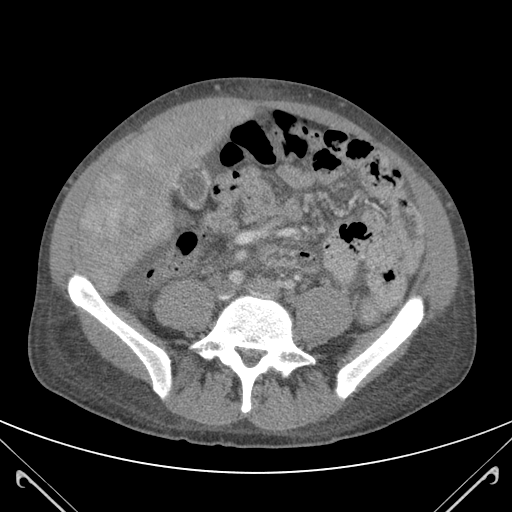
Contrast-enhanced abdominal CT (liver protocol), one axial slice. Slice 27 of 118 in the series (ordered by position). Soft-tissue window (W 400 / L 40 HU). 3 mm slice thickness. 512 × 512 image matrix, field of view 380 × 380 mm. Case-level facts recorded for this patient, not image findings: diagnosis: hepatocellular carcinoma (patient treated with transarterial chemoembolisation; whether this scan precedes or follows treatment is not stated here); TNM stage (as recorded): Stage-IIIB; Child-Pugh class: A; tumour nodularity: uninodular.
Annotated regions visible in this slice (semi-automatic segmentation, software-assisted and operator-edited):
- mass: bounding box [x1, y1, x2, y2] px = [79, 125, 186, 264]